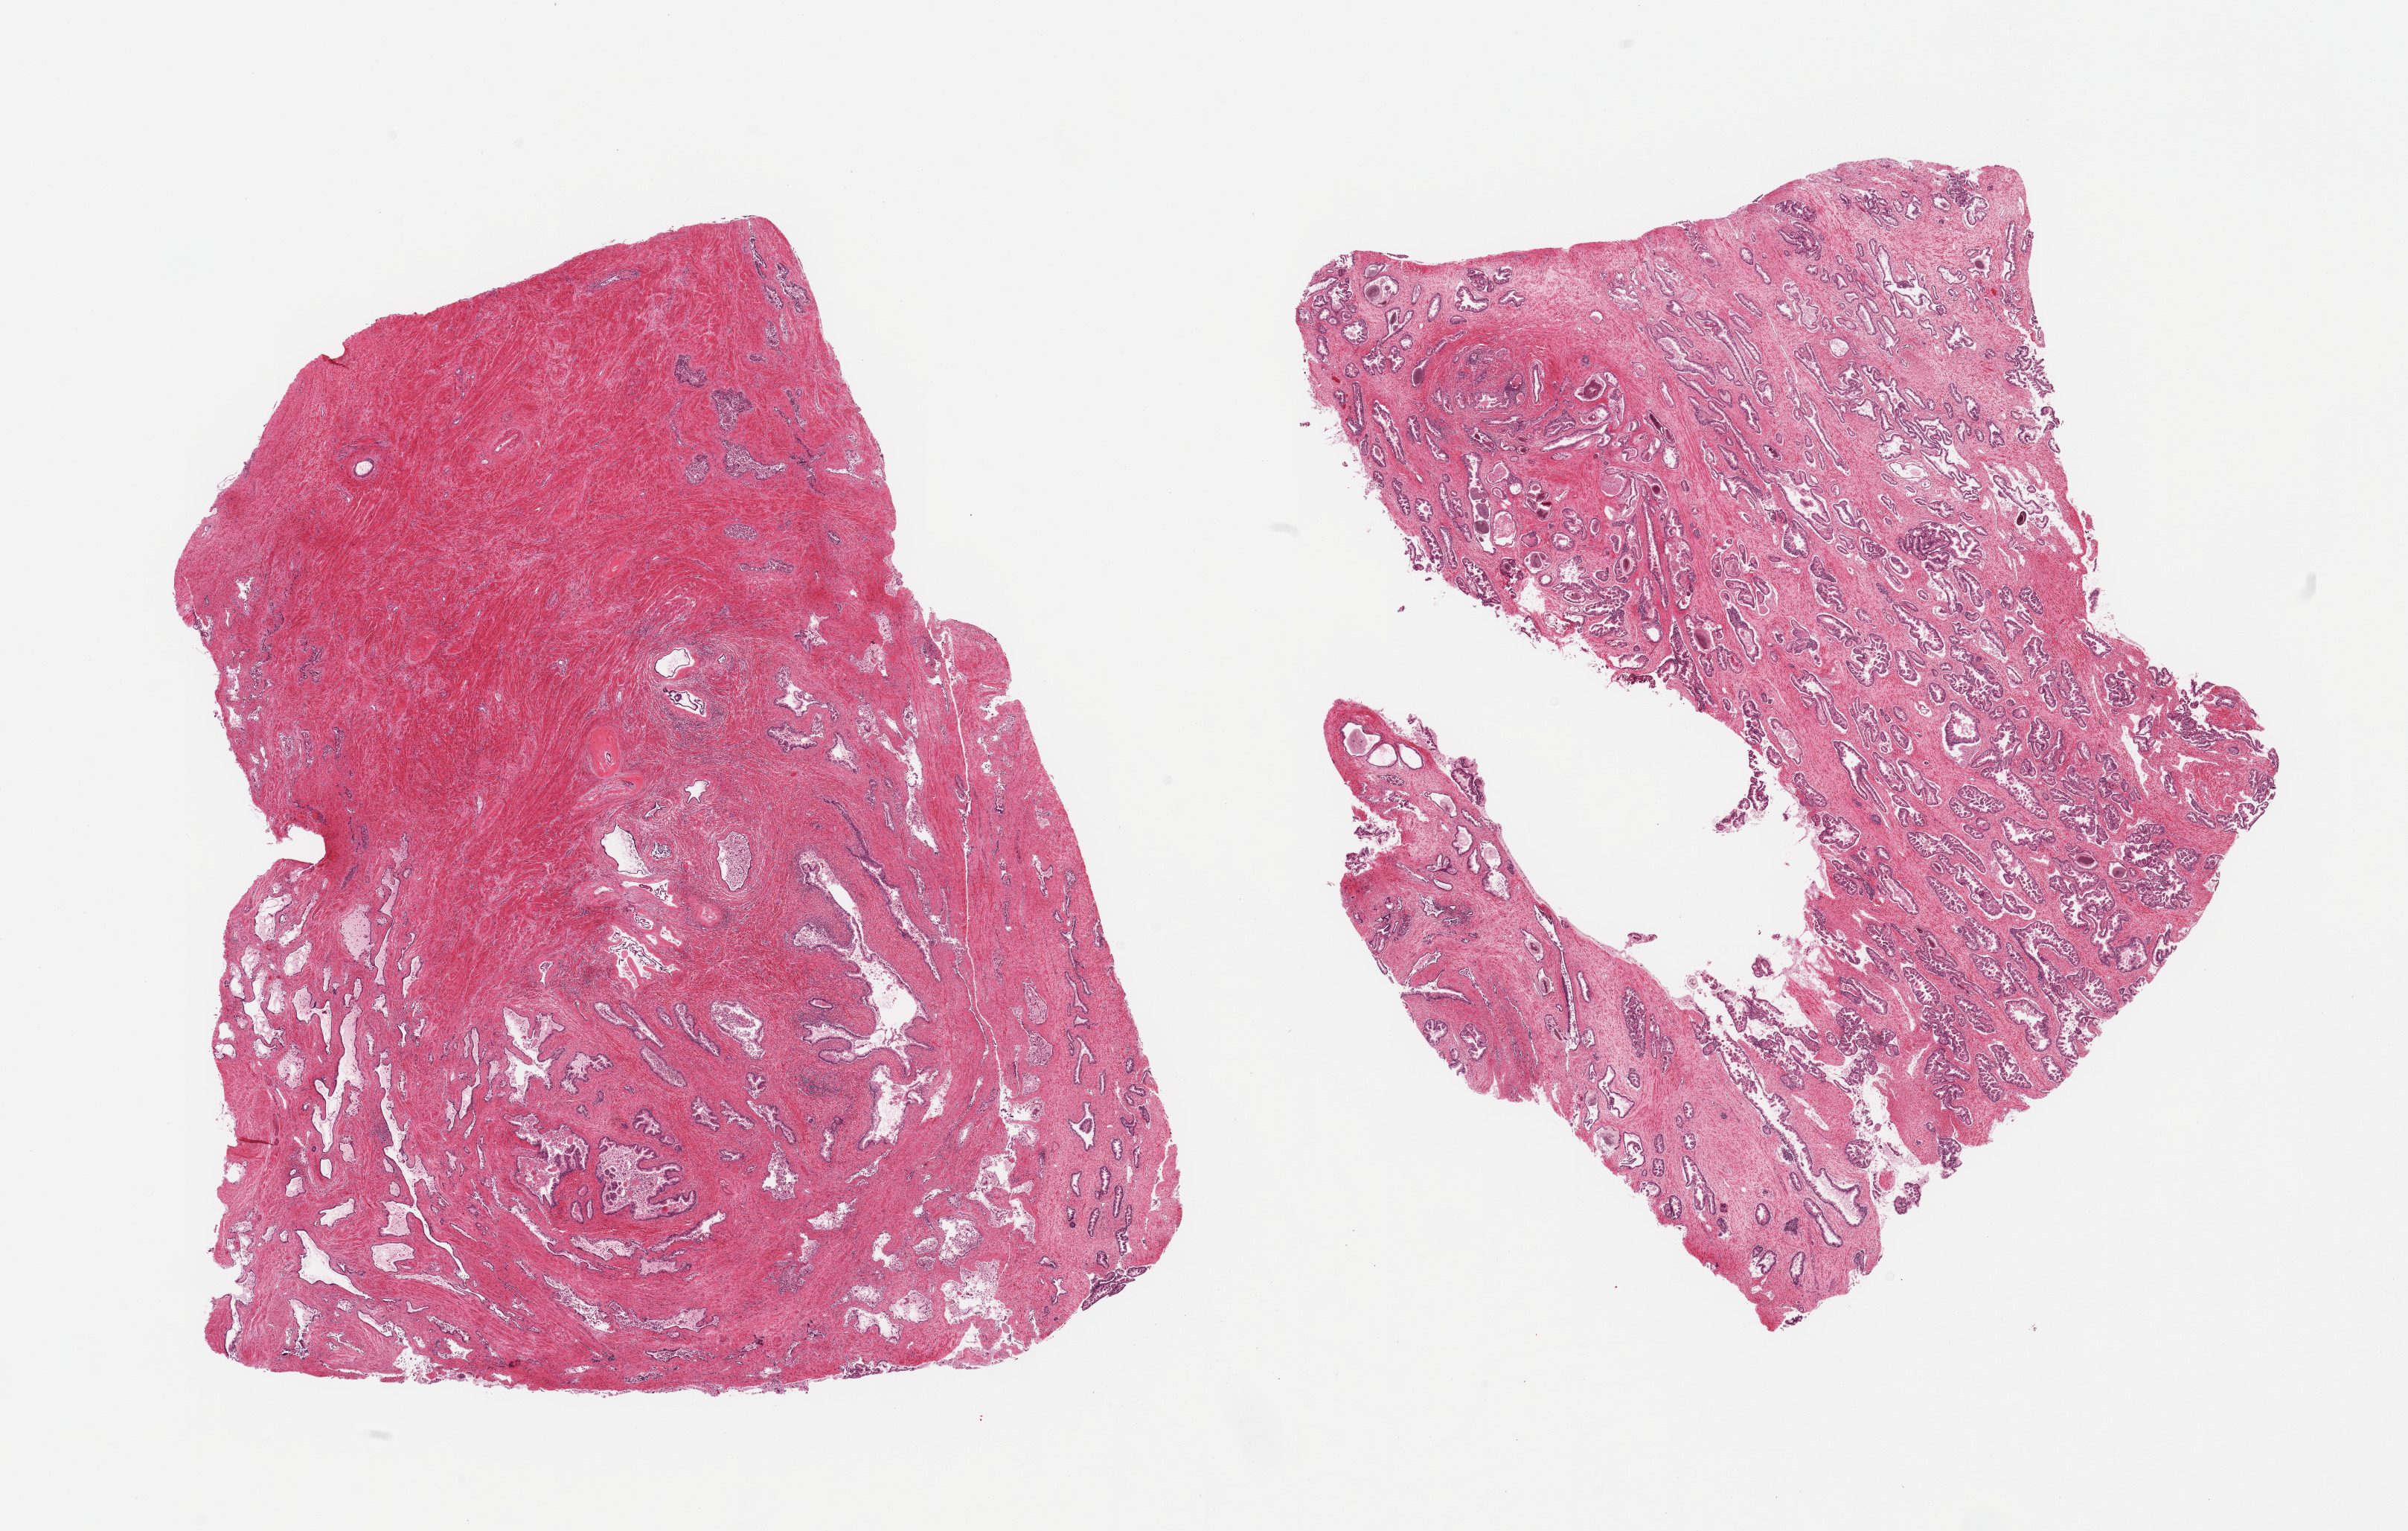
Digitized hematoxylin and eosin (H&E)-stained section, whole scanned area (about 25.6 x 16.3 mm) shown as a low-resolution overview, PAXgene-fixed, paraffin-embedded tissue, sampled site (target tissue): prostate, donor tissue sample. Donor sex: male.
* review note (as recorded): 2 pieces; one piece with 50% stromal hyperplasia devoid of glandular component; numerous corpora amylacea; sloughed glandular epithelium